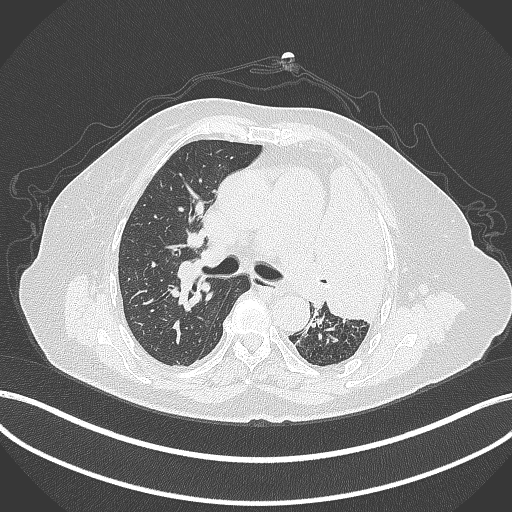
Chest CT, one axial slice; slice 243 of 399 in the series (ordered by position); 120 kVp; lung window (W 1500 / L -600 HU); 1 mm slice thickness; 512 × 512 image matrix. Female patient, age 75 years. From the clinical record (not read from this slice): clinical TNM (as recorded): T3 N3 M1.
Annotated regions visible in this slice (rectangle marked by the reading radiologist):
- lung tumour (recorded histology: adenocarcinoma): bounding box [x1, y1, x2, y2] px = [323, 161, 392, 324]